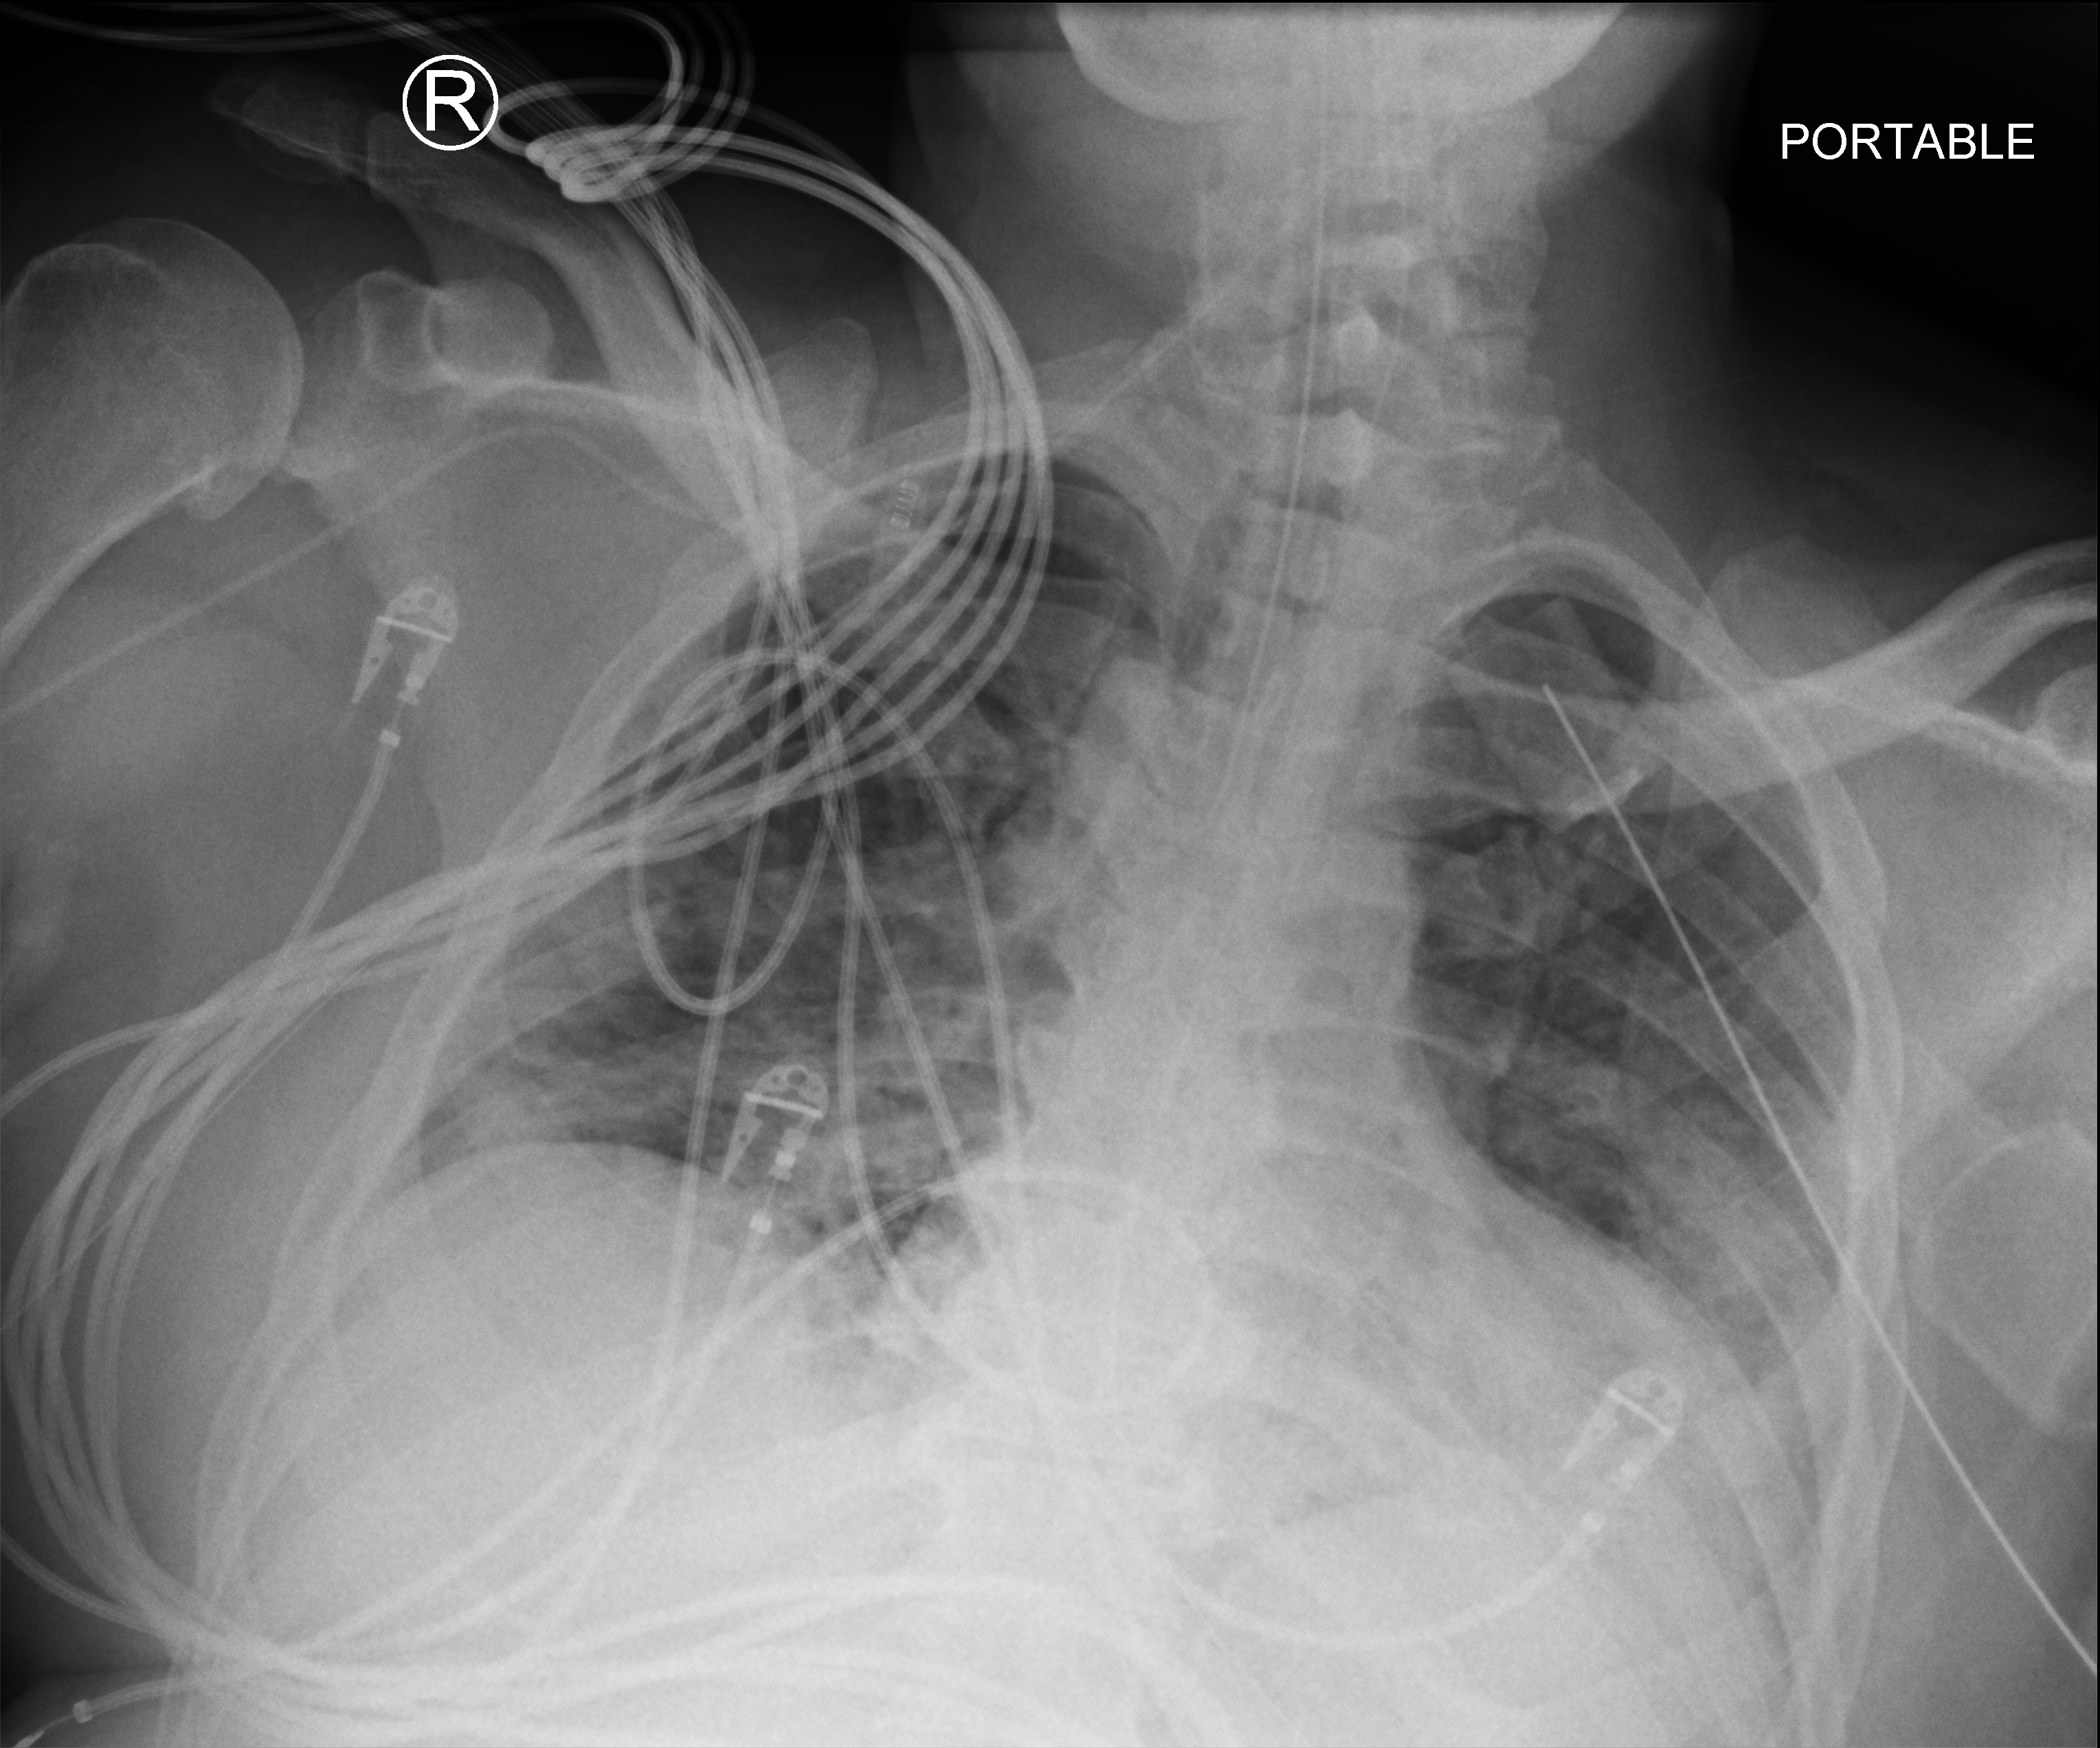
Bedside chest radiograph (computed radiography); anteroposterior (AP) projection. Male patient hospitalised with COVID-19, age 18–59 years.
Admission-level facts for this patient (not findings on this image; timing relative to this image not recorded): admitted to intensive care during this hospital stay: yes.